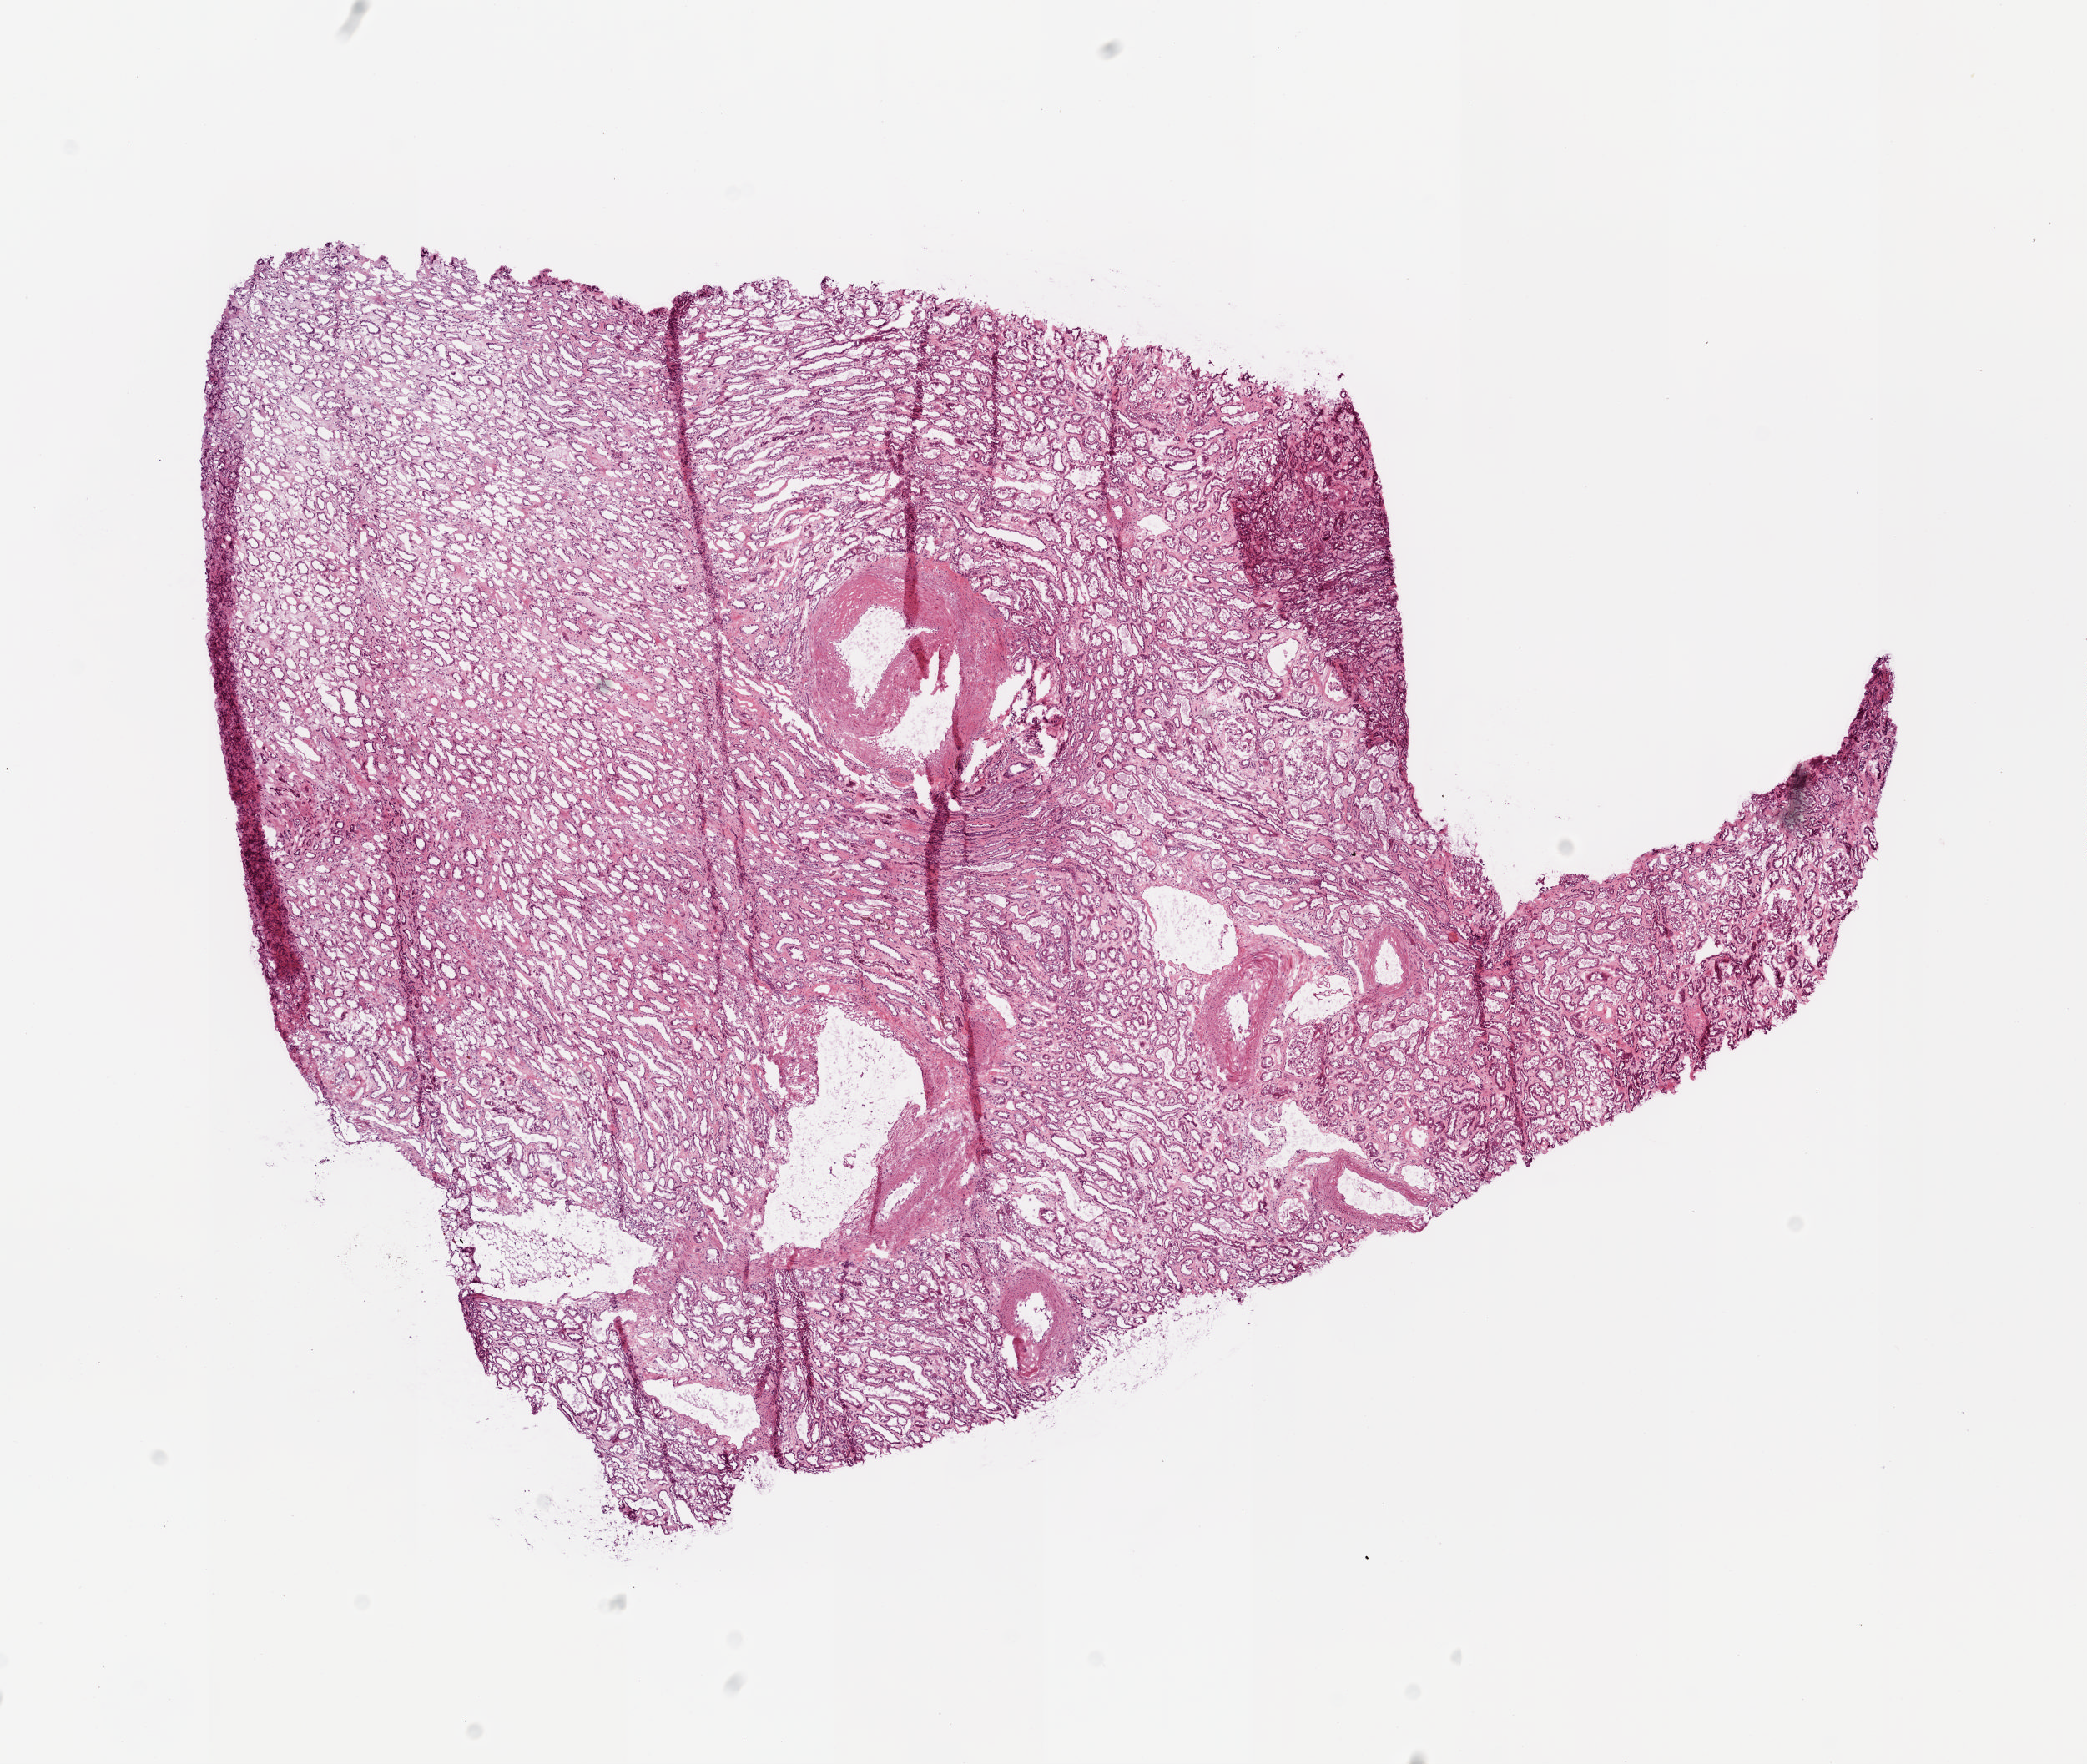
Whole-slide histology image, H&E-stained — a low-resolution overview of the entire scanned area, about 9.9 x 8.4 mm, frozen section from the top of the tissue portion, sample: solid tissue normal (non-tumour tissue), kidney. Patient: male, age at initial diagnosis 79 years.
* this section: solid tissue normal sample (biorepository sample class)
* patient diagnosis: Clear cell adenocarcinoma, NOS